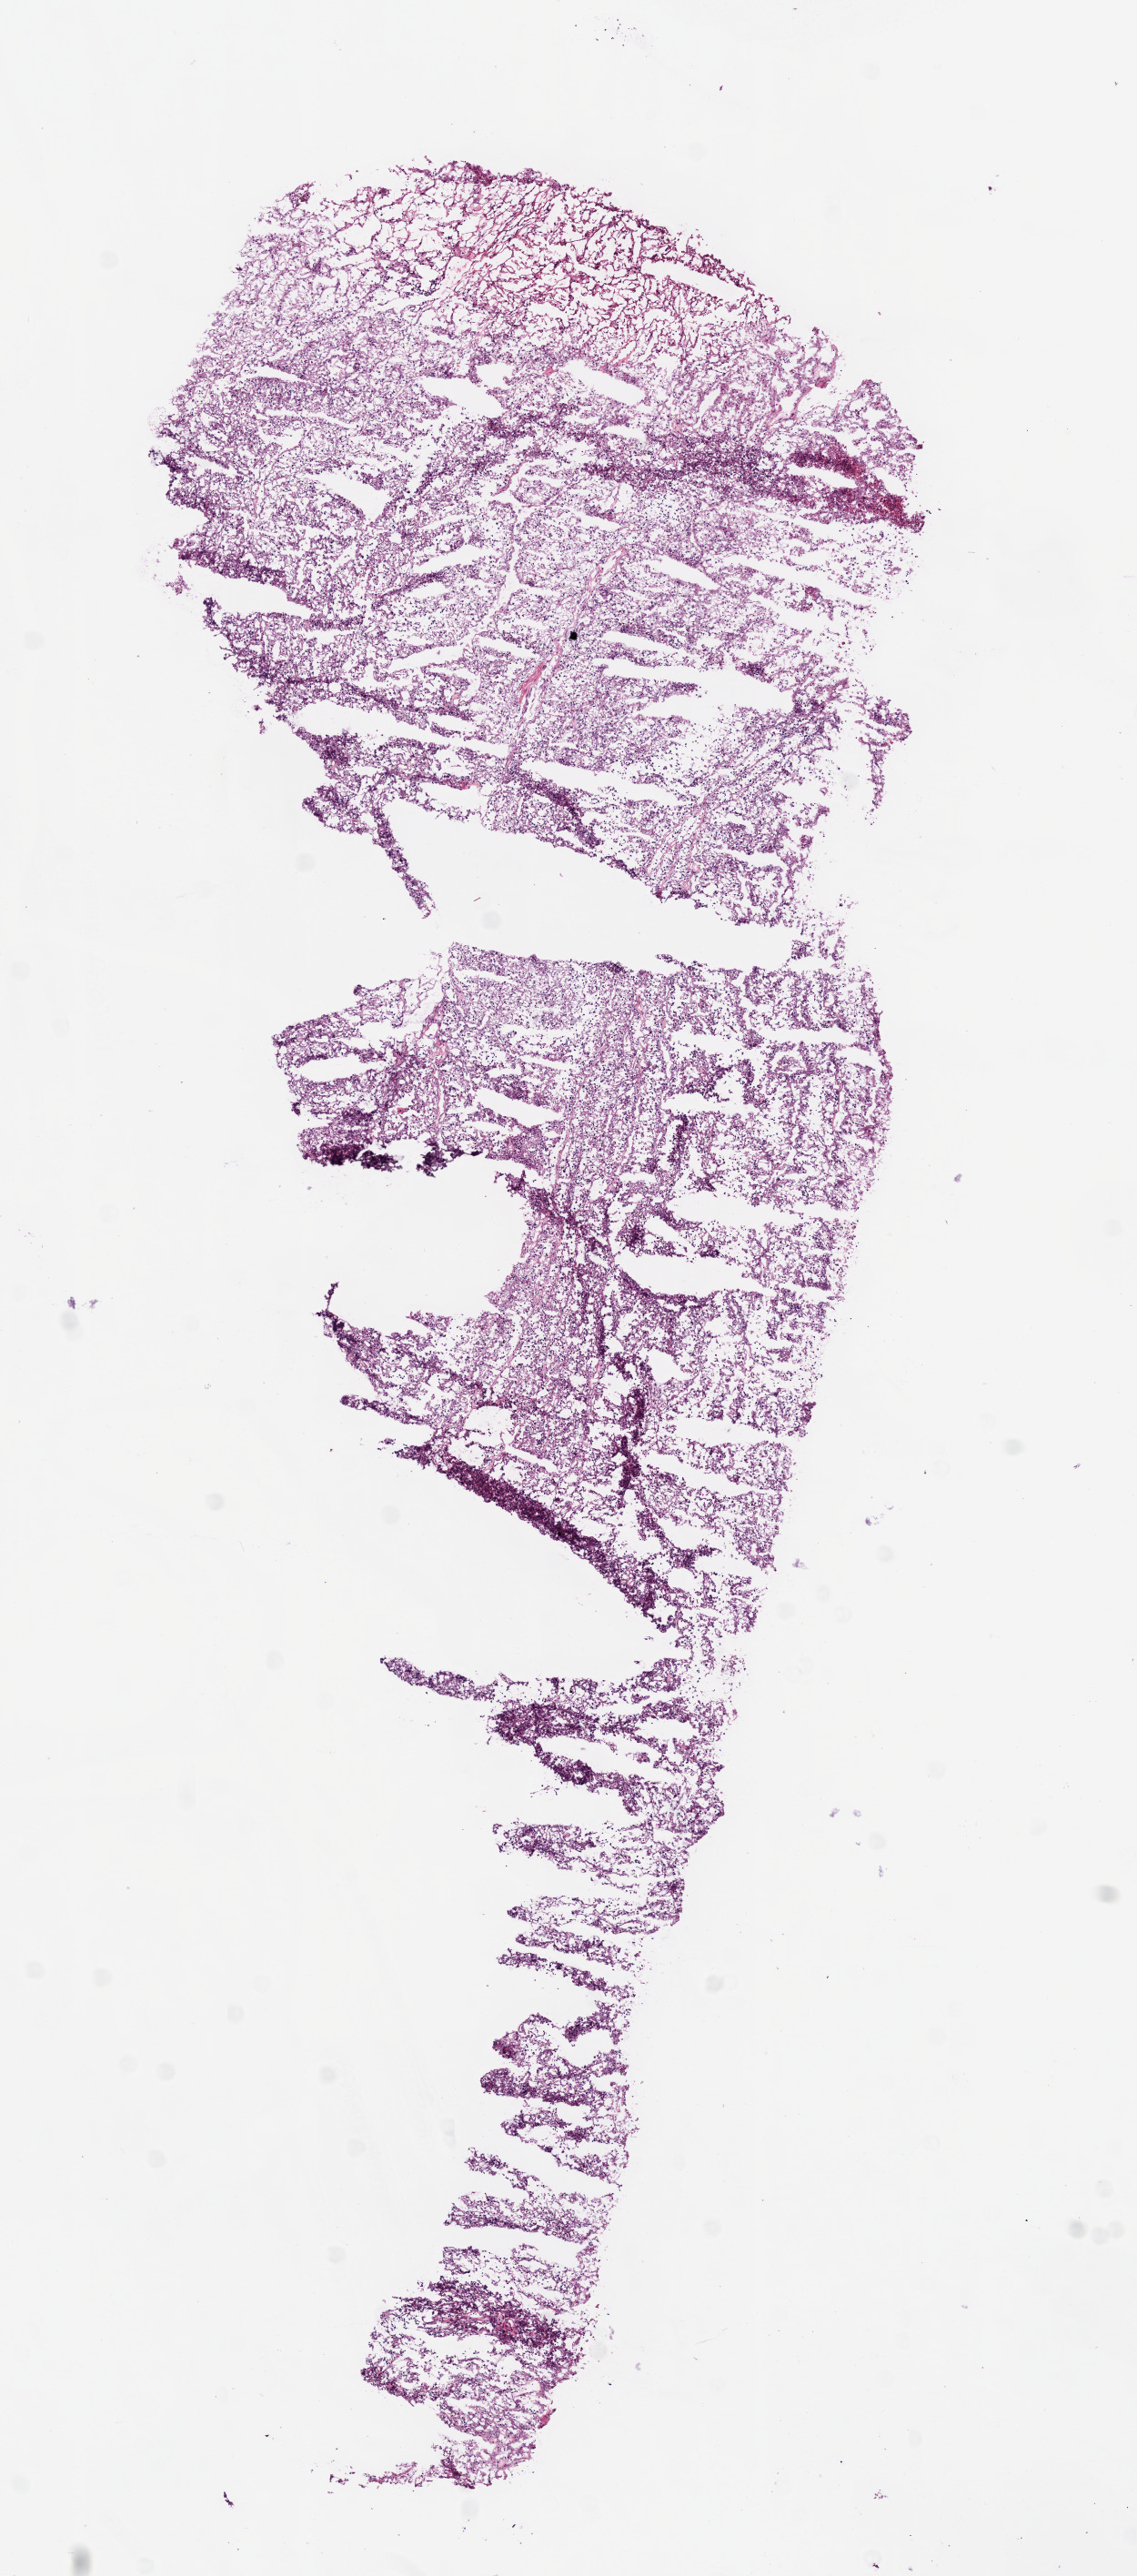
Whole-slide histology image, H&E — whole scanned area (about 5.0 x 11.4 mm) shown as a low-resolution overview; frozen section from the bottom of the tissue portion; kidney, primary tumour sample. Male patient; age at initial diagnosis 61 years. Histologic grade: G3 (poorly differentiated). Pathologist review of this section (percent, as recorded): tumour cells 95%, tumour nuclei 80%, normal cells 0%, stromal cells 5%, necrosis 0%.
• AJCC pathologic stage: III
• laterality: left
• lymph nodes positive (case pathology): 3 of 8 examined
• diagnosis: Clear cell adenocarcinoma, NOS